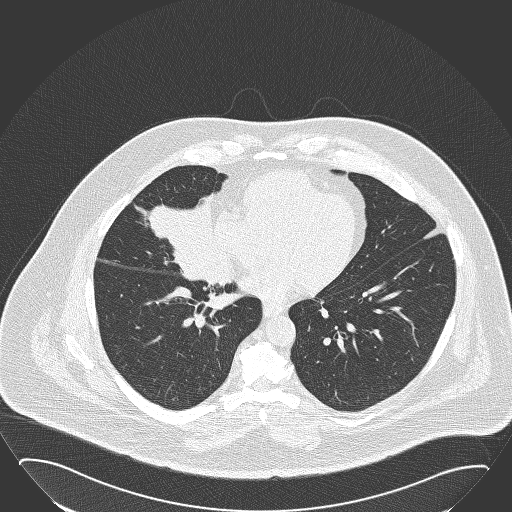
Low-dose screening chest CT, one axial slice; position 71 of 168 along the scan axis; 120 kVp; lung window (W 1500 / L -600 HU); 2 mm slice thickness; 512 × 512 image matrix.
Annotated regions visible in this slice (manually delineated by an expert):
- lesion 1 (tumor, hilum of right lung): bounding box (x1, y1, x2, y2) in pixels: (149, 195, 231, 287)